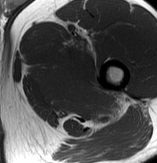
MRI of an extremity soft-tissue mass, one axial slice. Slice 65 of 70 in the series (ordered by position). MR volume resampled by the dataset authors to the PET/CT grid (not the native acquisition matrix). 3.27 mm slice thickness. 157 × 163 image matrix, field of view 153 × 159 mm. Male patient. From the clinical record (not read from this slice): histological type: extraskeletal osteosarcoma; grade: high; site of the primary tumour: left adductur.
Structures marked on this image (expert contour drawn on MRI and transferred to this co-registered scan by the dataset authors):
- gross tumour volume (mass): bounding box <28,26,130,125> (left, top, right, bottom; pixels)